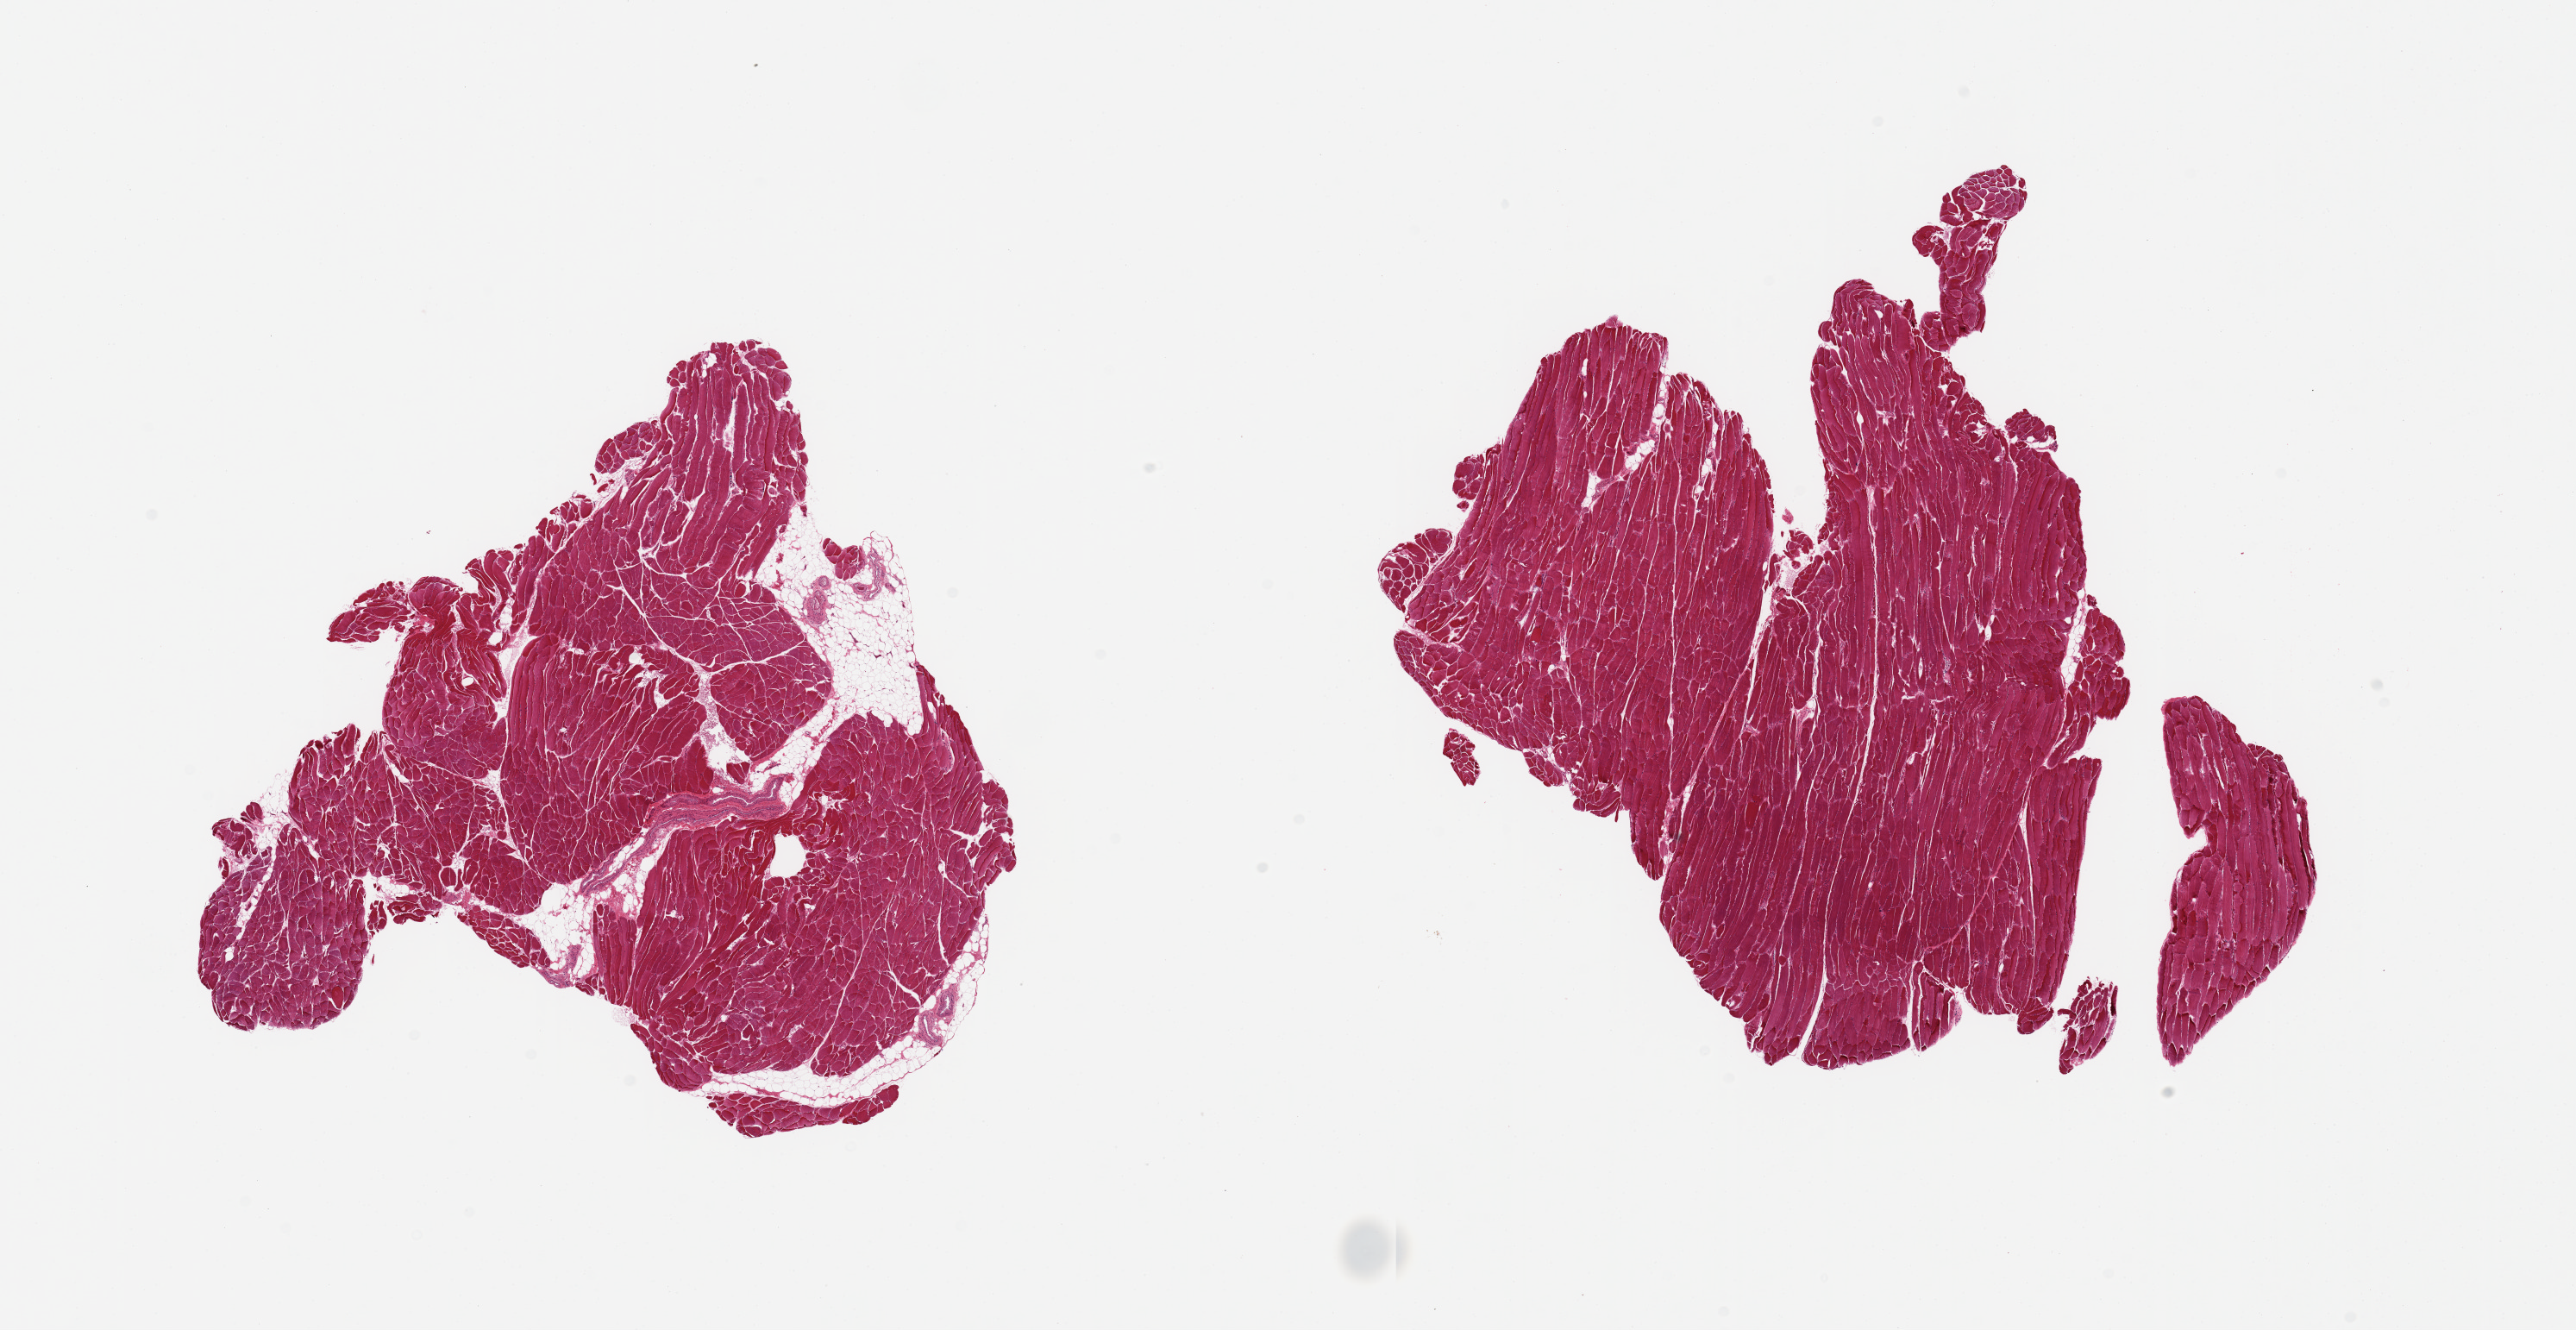
Hematoxylin and eosin (H&E) whole-slide image, brightfield — low-resolution overview of the scanned area, about 23.6 x 12.2 mm. PAXgene-fixed paraffin-embedded (PFPE) section. Sampled site (target tissue): skeletal muscle. Donor tissue sample.
Pathologist's review note for this sample: 2 pieces, interstitial fat up to ~10%.